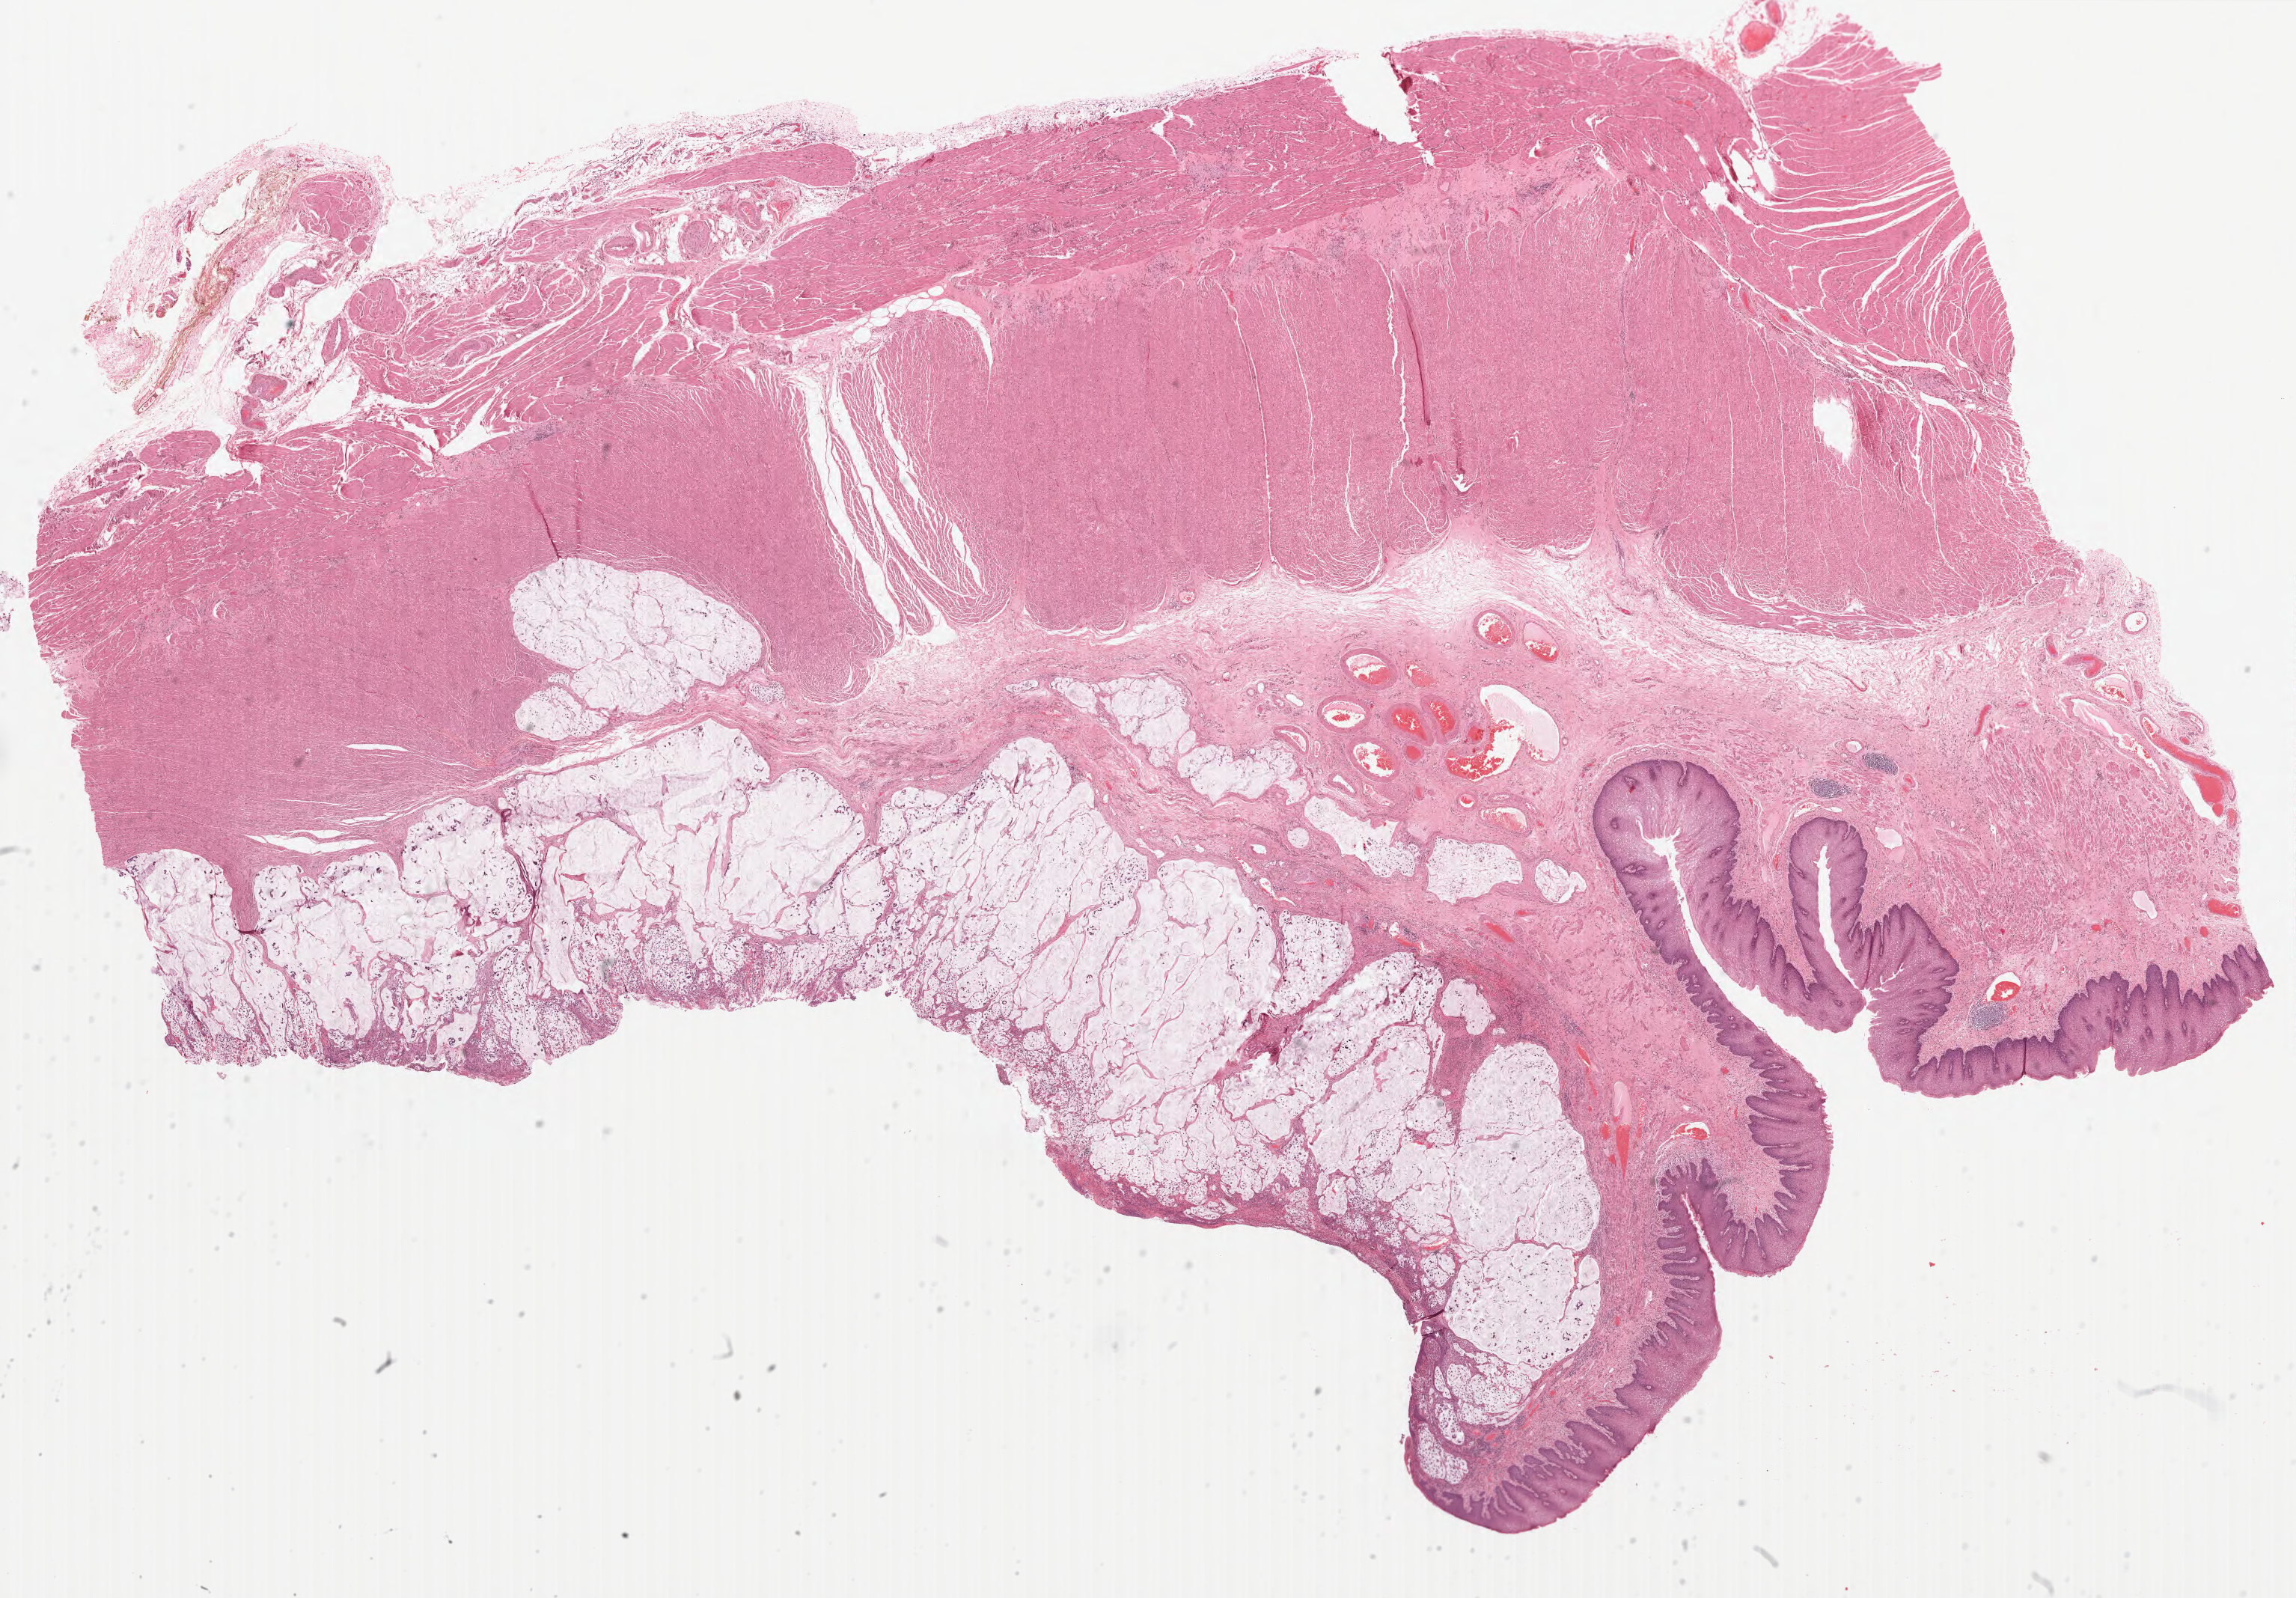
Whole-slide histology image, H&E-stained — low-resolution overview of the scanned area, about 24.7 x 17.2 mm; formalin-fixed paraffin-embedded (FFPE) diagnostic section; stomach, primary tumour sample. Patient: male, age at initial diagnosis 68 years. Histologic grade: G1 (well differentiated).
Pathologic diagnosis: Signet ring cell carcinoma (cardia, NOS). Lymph nodes positive (case pathology): 0 of 32 examined. TNM: T2 N0 M0. AJCC pathologic stage: IB (7th edition).